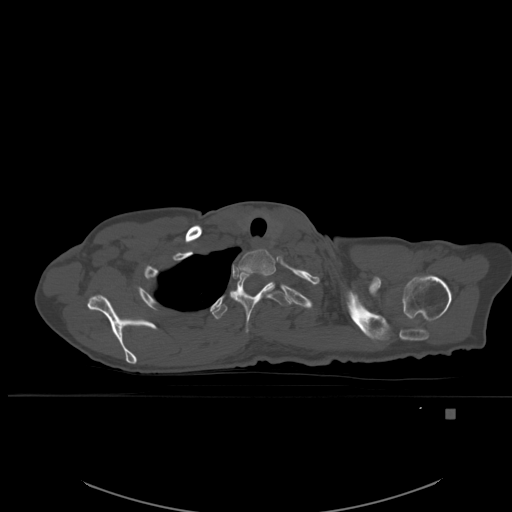
CT including the spine, one axial slice. Slice 438 of 537 in the series (ordered by position). Bone window (W 1800 / L 400 HU). 512 × 512 image matrix, field of view 440 × 440 mm. Female patient, age 45 years. From the clinical record (not read from this slice): primary cancer: lung.
Outlined on this slice (semi-automatic segmentation, software-assisted and operator-edited):
- T1 vertebra: box from (x=234, y=249) to (x=276, y=279) px
- T2 vertebra: (x=229, y=272)–(x=290, y=334)
- T3 vertebra: (x=212, y=301)–(x=228, y=320)